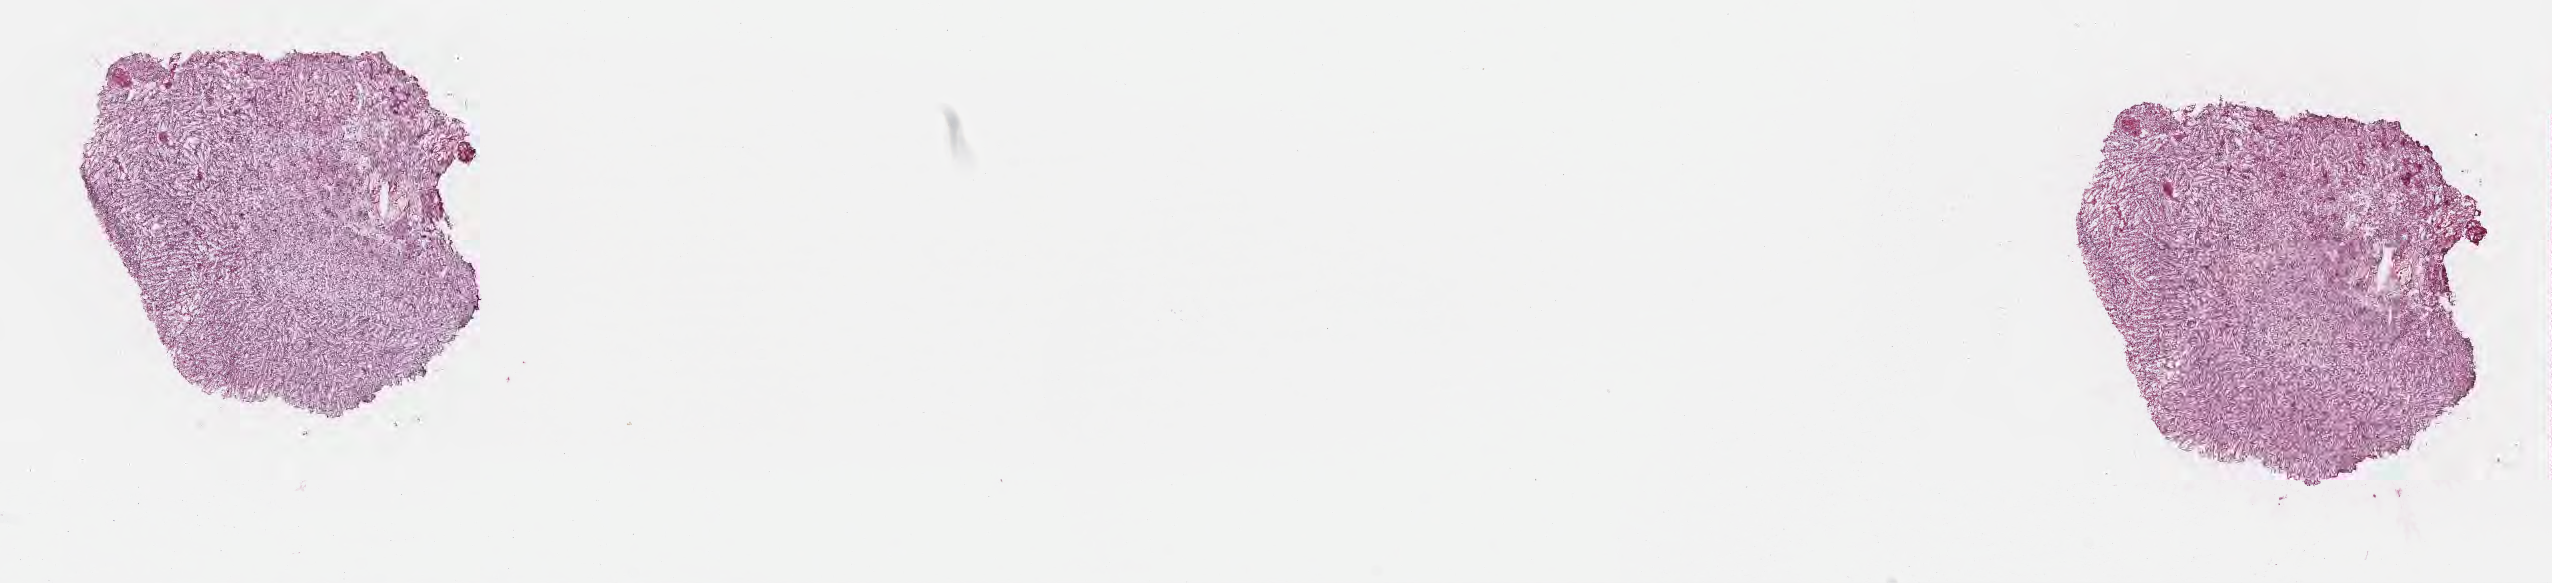
Whole-slide image, hematoxylin and eosin (H&E) stain — whole scanned area (about 20.6 x 4.7 mm) shown as a low-resolution overview. Frozen section. Specimen: primary tumor. Site: brain. Patient: male. Pathologist review of this section (percent, as recorded): tumor cells 48%, tumor nuclei 68%, stromal cells 30%, necrosis 0%, normal cells 22%. Inflammatory infiltration, as recorded: lymphocyte infiltration 0%, monocyte infiltration 0%, neutrophil infiltration 0%.
- section: top of the tissue portion
- diagnosis: Glioblastoma, NOS